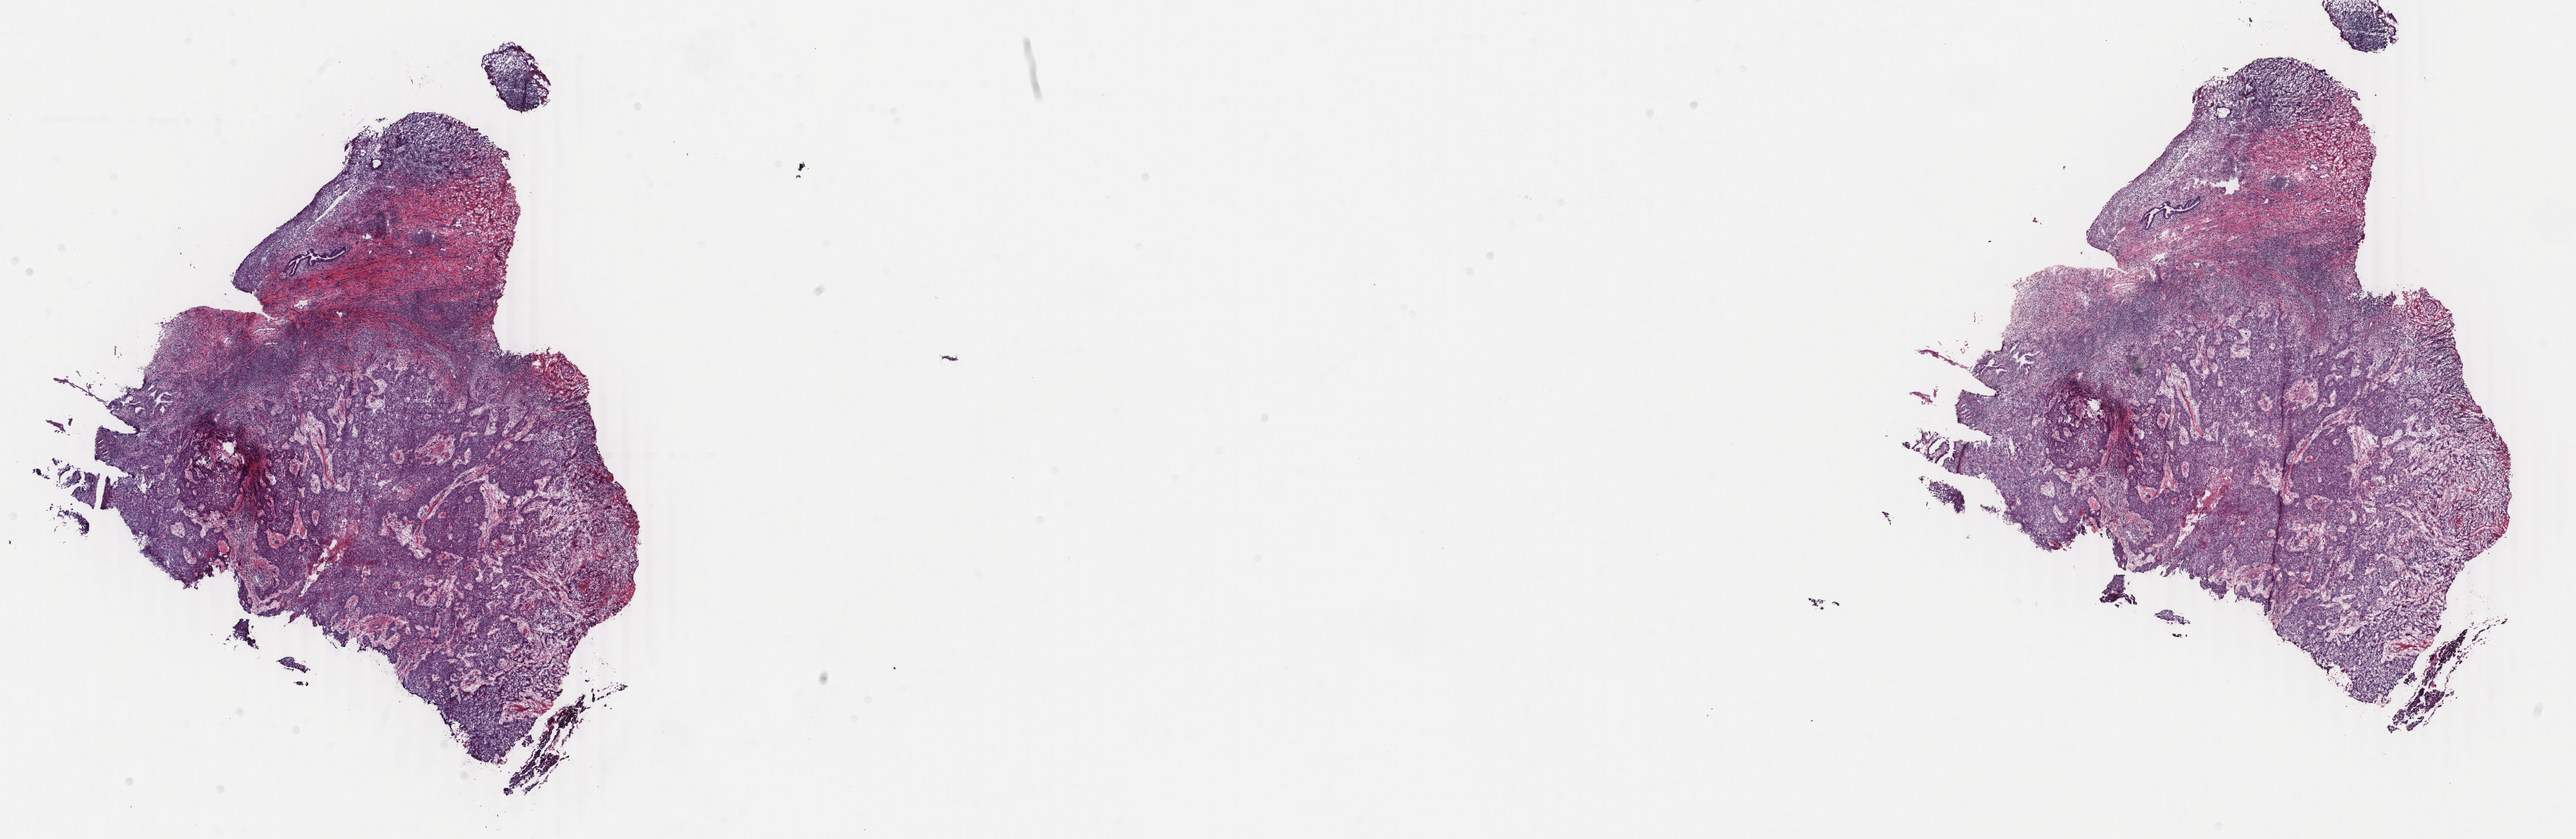
Digitized H&E tissue section (whole slide), whole scanned area (about 26.7 x 8.7 mm, acquisition: 40x scan) shown as a low-resolution overview; frozen section; sample: primary tumour, cervix. Patient: female, age at initial diagnosis 48 years.
Histologic diagnosis: Squamous cell carcinoma, NOS.